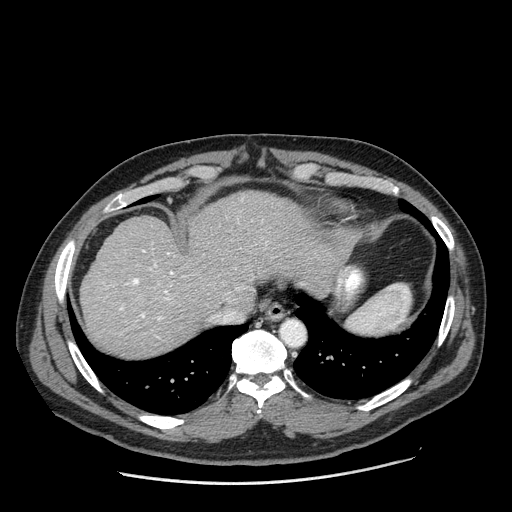
Contrast-enhanced abdominal CT (liver protocol), one axial slice; slice 159 of 198 in the series (ordered by position); reconstruction kernel STANDARD; 120 kVp; one of 2 acquisitions stored at this slice position; soft-tissue window (W 400 / L 40 HU); 2.5 mm slice thickness; 512 × 512 image matrix, field of view 400 × 400 mm. From the clinical record (not read from this slice): diagnosis: hepatocellular carcinoma (patient treated with transarterial chemoembolisation; whether this scan precedes or follows treatment is not stated here); TNM stage (as recorded): Stage-II; Child-Pugh class: A; tumour differentiation: moderately differentiated; tumour nodularity: multinodular.
Outlined on this slice (semi-automatically segmented with operator editing):
- abdominal aorta: bounding box <282,322,303,344> (left, top, right, bottom; pixels)
- liver parenchyma outside the tumour (the mass and vessels are separate outlines, so this box may not span the whole liver): <80,190,353,356>
- liver vessels: <120,250,238,338>